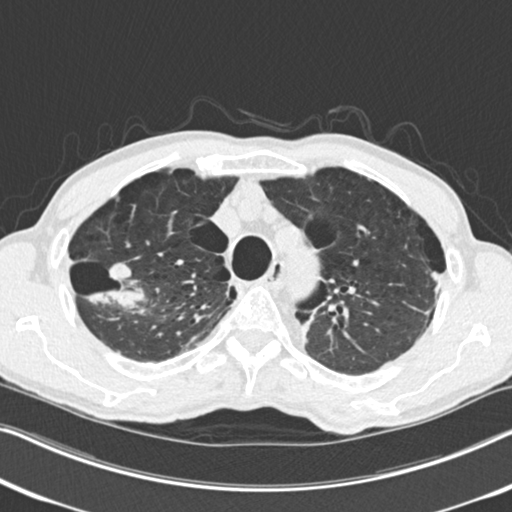
Axial slice from a low-dose chest CT screening exam, second annual screen, lung window (W 1500 / L -600 HU), slice 57 of 251 in the series. Male participant, aged 71 years at enrolment. Current smoker at enrolment.
Expert-annotated lung lesion, bounding box [x1, y1, x2, y2] px = [75, 253, 149, 320]. The screening reader recorded 4 non-calcified nodules or masses ≥4 mm on this exam (right upper lobe, right upper lobe, right upper lobe, left upper lobe); which of them this box marks is not recorded. Official screen result: positive, change unspecified: nodule(s) >= 4 mm or enlarging nodule(s), mass(es), or other non-specific abnormalities suspicious for lung cancer. Participant outcome: lung cancer diagnosed 83 days after this screen — adenocarcinoma, NOS, right upper lobe, well differentiated (G1), stage IA (AJCC 6th edition), 30 mm at pathology.